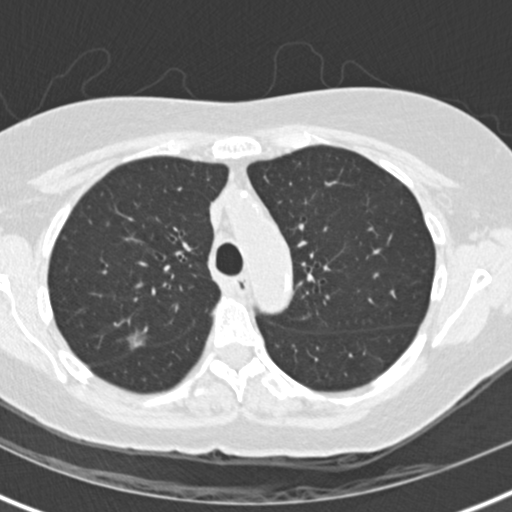
Axial slice from a low-dose chest CT screening exam. Baseline annual screen. Lung window (W 1500 / L -600 HU). 2 mm slice thickness. Standard (soft-tissue) reconstruction kernel (B30f). Slice 47 of 147 in the series. 512 × 512 image matrix, field of view 300 × 300 mm. Female, age 72 years at enrolment.
- Expert reader's lesion annotation, bounding box [x1, y1, x2, y2] px = [108, 312, 170, 368].
- The exam's reader record, not a measurement of the box and not confirmed to be the same lesion: non-calcified nodule or mass ≥4 mm, right upper lobe, 11 × 11 mm, poorly defined margins, ground glass attenuation.
- Official screen result: positive, change unspecified: nodule(s) >= 4 mm or enlarging nodule(s), mass(es), or other non-specific abnormalities suspicious for lung cancer.
- Lung cancer was diagnosed 75 days after this screen: bronchiolo-alveolar adenocarcinoma, NOS, right upper lobe, well differentiated (G1), stage IA (AJCC 6th edition), 23 mm at pathology.